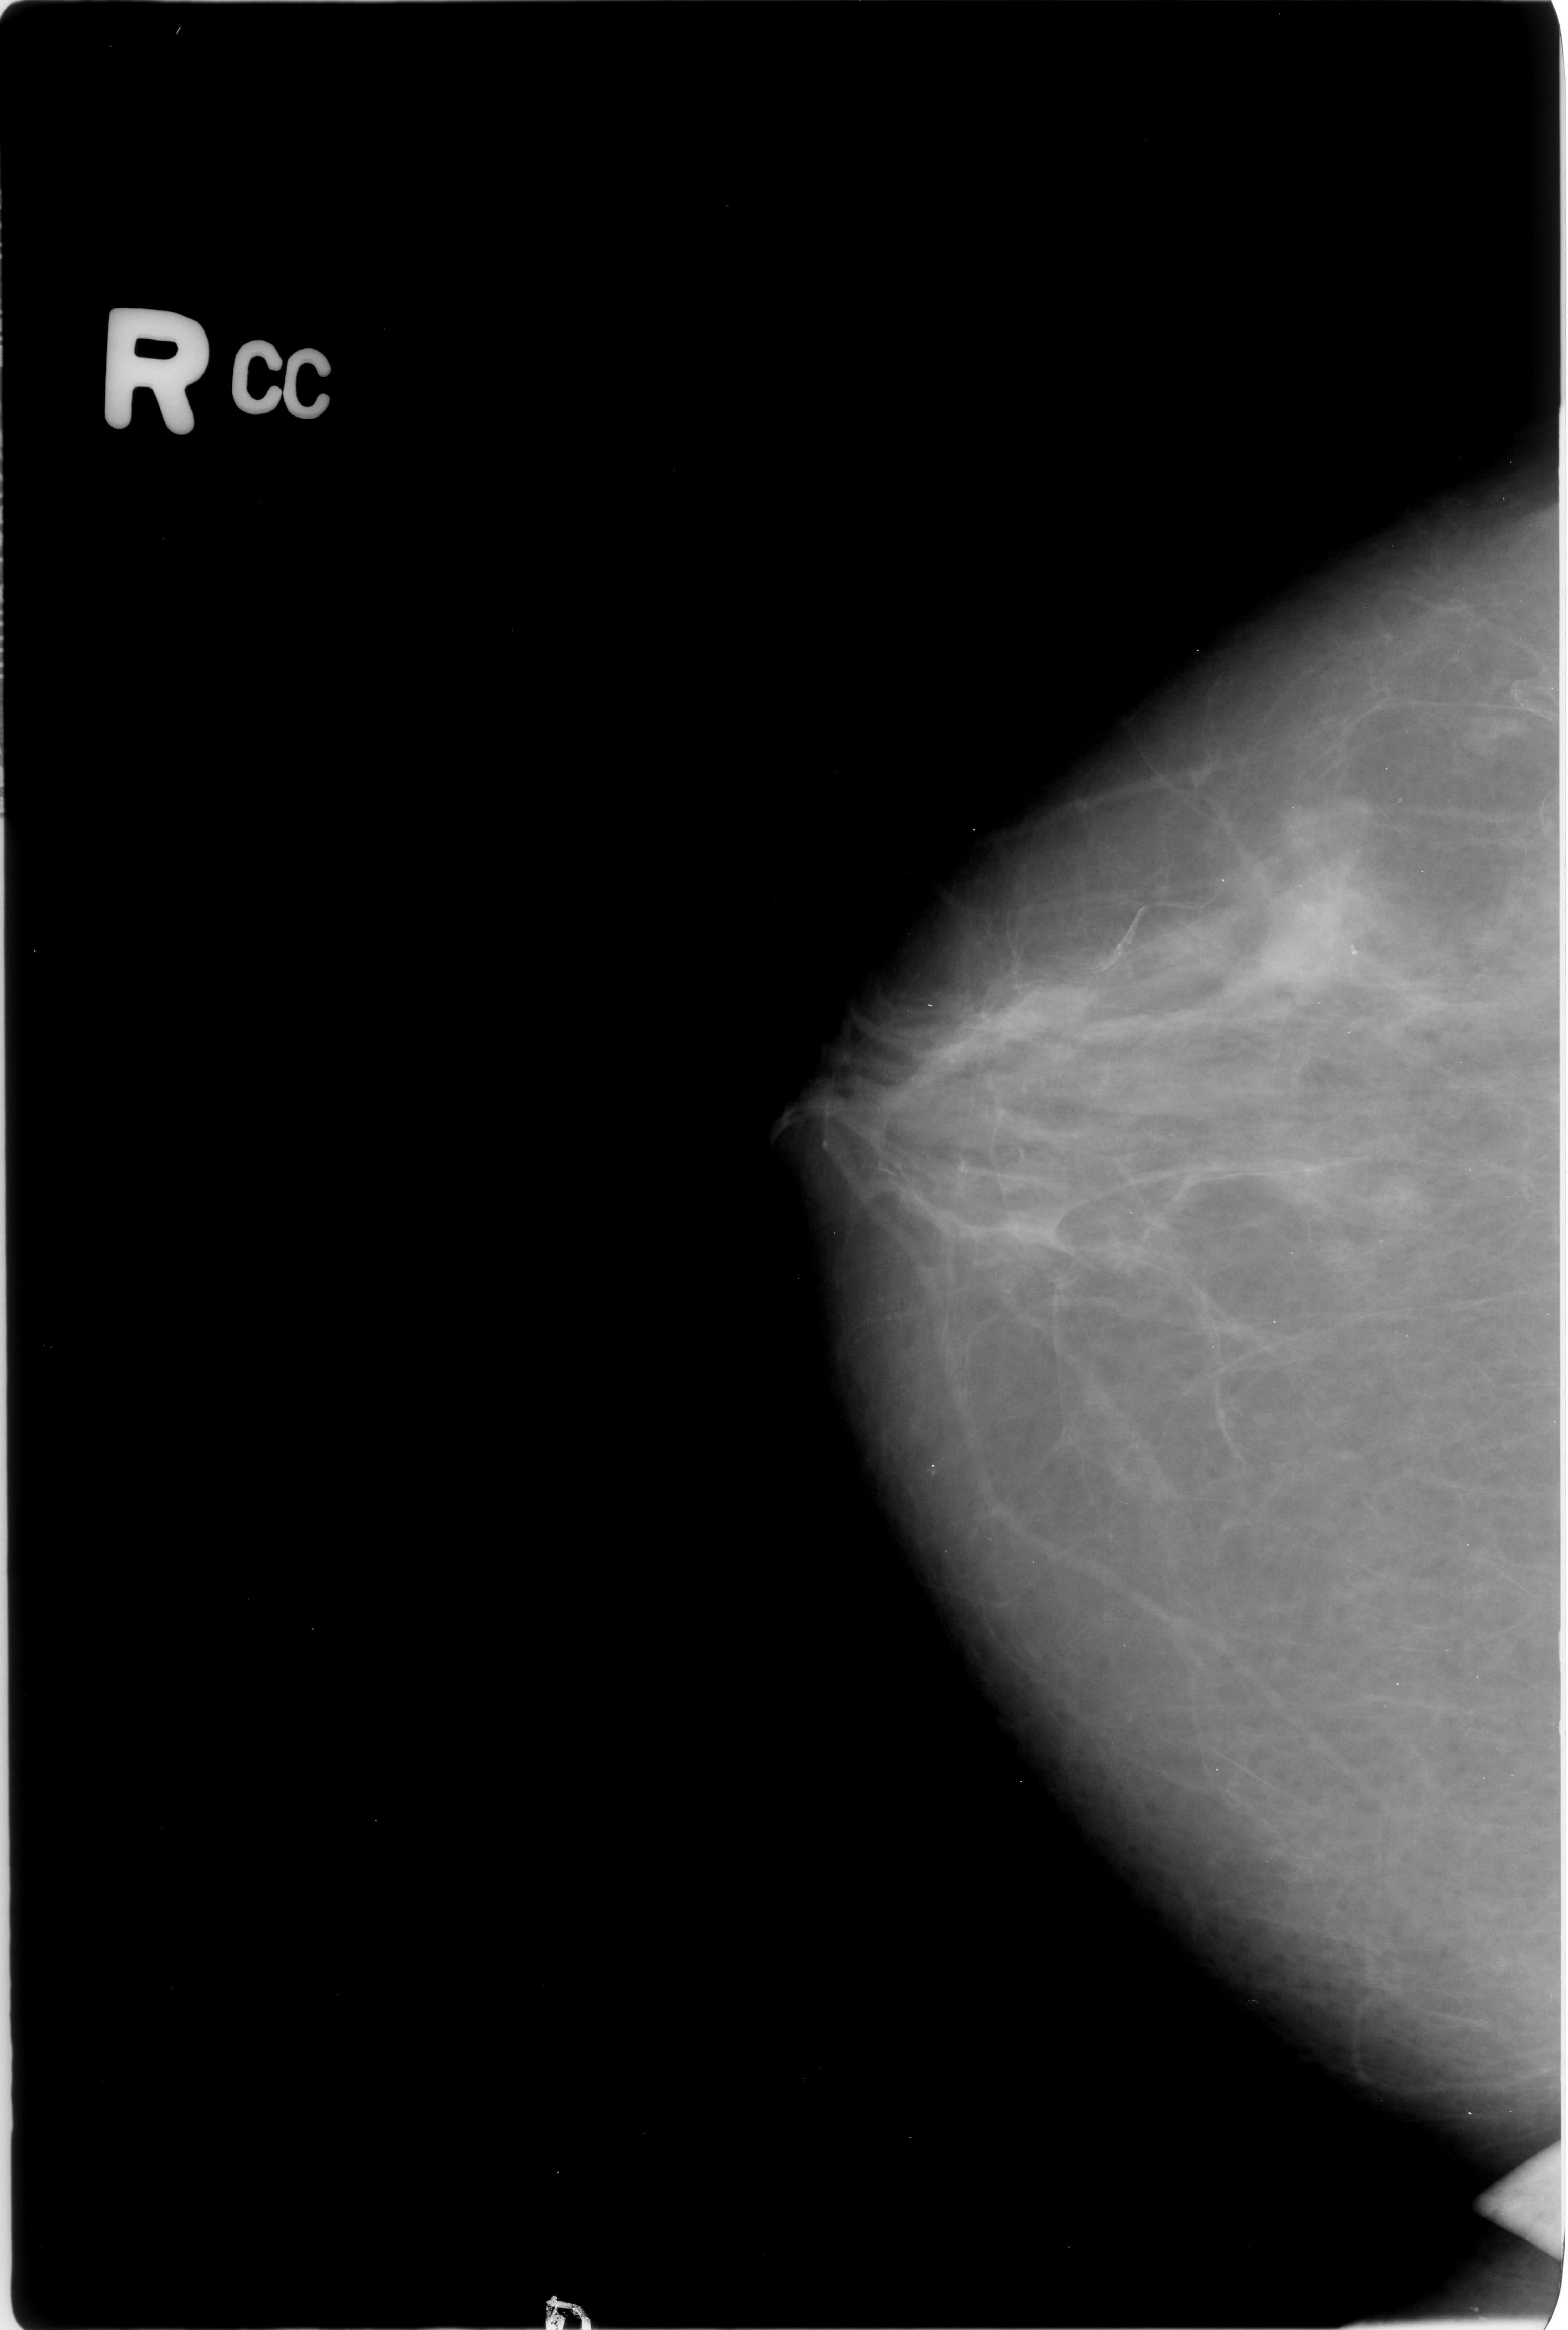
Scanned film-screen mammogram, right breast, CC view, BI-RADS breast density category 2 (scale 1–4).
- Marked abnormality: mass, shape lobulated, margins obscured / ill defined; BI-RADS assessment category 3; pathology result (as recorded, not read from the image): malignant.